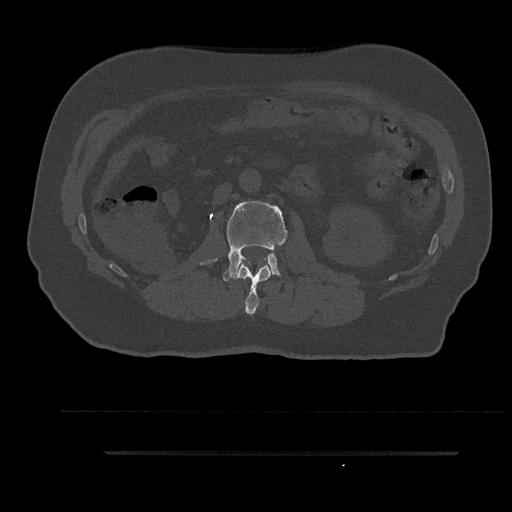
CT including the spine, one axial slice. Position 132 of 797 along the scan axis. 120 kVp. Bone window (W 1800 / L 400 HU). 0.5 mm slice thickness. 512 × 512 image matrix. Male patient, age 63 years. Case-level facts recorded for this patient, not image findings: primary cancer: renal; vertebrae with lytic lesions (as recorded): T8.
Annotated regions visible in this slice (semi-automatic segmentation, software-assisted and operator-edited):
- L1 vertebra: bounding box <234,262,272,315> (left, top, right, bottom; pixels)
- L2 vertebra: <201,201,288,281>